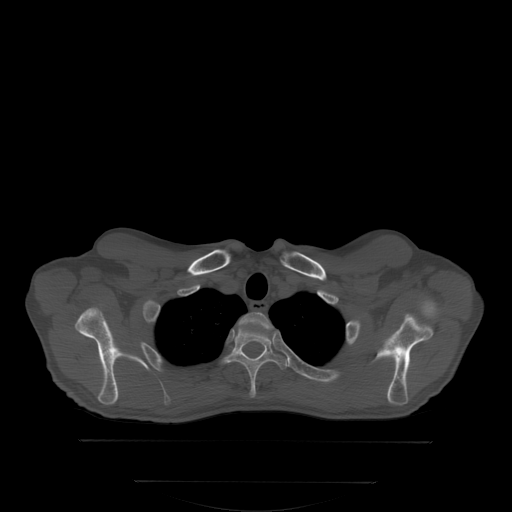
CT including the spine, one axial slice; bone window (W 1800 / L 400 HU); 2.5 mm slice thickness; 512 × 512 image matrix, field of view 500 × 500 mm. Male patient, age 58 years. From the clinical record (not read from this slice): primary cancer: prostate; vertebrae with lytic lesions (as recorded): L1.
Annotated regions visible in this slice (semi-automatically segmented with operator editing):
- T1 vertebra: bounding box (x1, y1, x2, y2) in pixels: (239, 312, 278, 338)
- T2 vertebra: (221, 322, 287, 396)
- T3 vertebra: (240, 351, 289, 364)